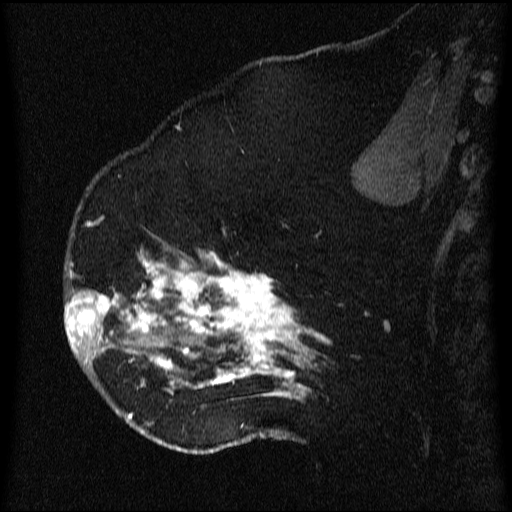
Breast MRI (dynamic contrast-enhanced), one sagittal slice; slice 41 of 64 in the series (ordered by position); dynamic contrast-enhanced series, image 2 of 3 at this slice position (ordered by acquisition); 1.5 T; TE 4.2 ms, TR 9.1 ms; 2.2 mm slice thickness; 512 × 512 image matrix, field of view 180 × 180 mm. Patient: female, 52 years.
Outlined on this slice (semi-automatic segmentation, software-assisted and operator-edited):
- analysis volume of interest (the breast-tissue region the enhancement analysis was run in; not a lesion): bounding box (x1, y1, x2, y2) in pixels: (65, 203, 331, 438)
- tumour enhancement mask (voxels above the 70 % enhancement threshold inside the analysis volume of interest): (65, 223, 327, 438)